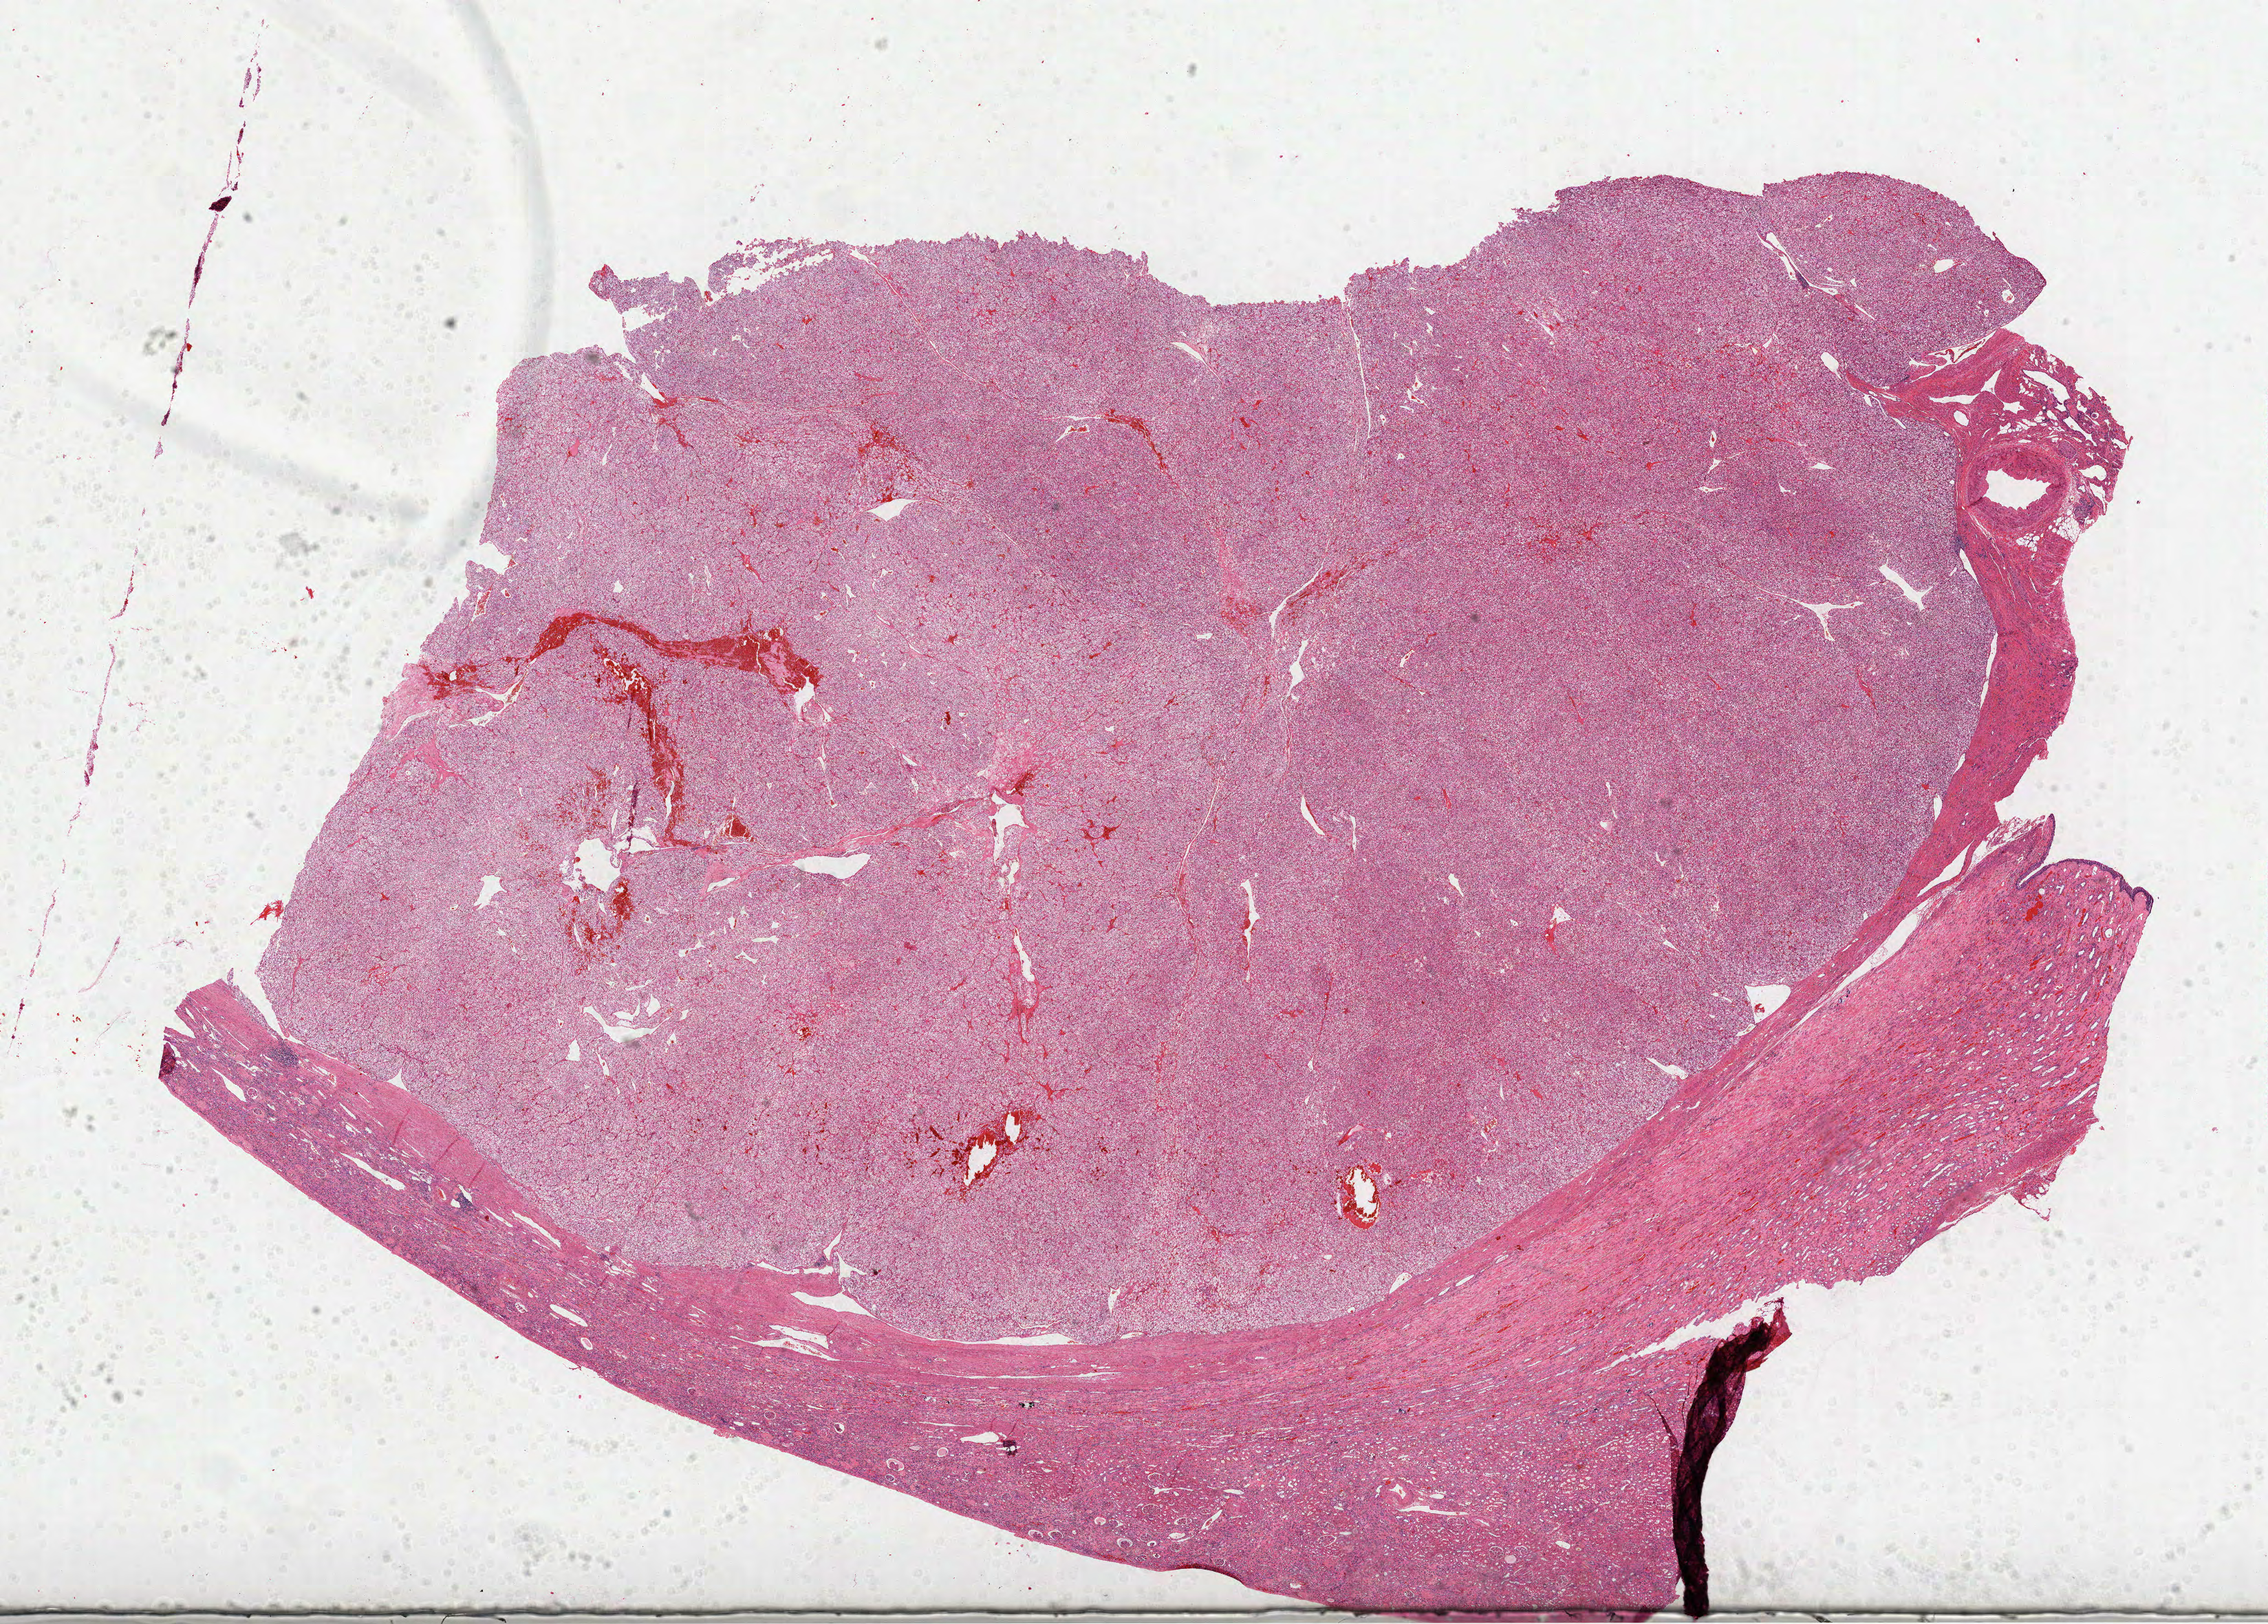
Digitized Hematoxylin and eosin (H&E) stained tissue section (whole slide), whole scanned area (about 26.6 x 19.0 mm) shown as a low-resolution overview. FFPE section. Primary tumour sample from the kidney. Patient: female, age at initial diagnosis 88 years. Histologic grade: G3 (poorly differentiated).
AJCC pathologic stage: III. Laterality: right. Histologic diagnosis: Clear cell adenocarcinoma, NOS.